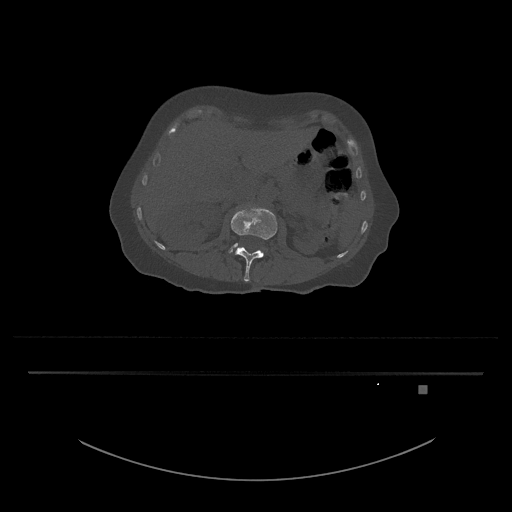
CT including the spine, one axial slice; slice 480 of 797 in the series (ordered by position); reconstruction kernel Br40s/3; bone window (W 1800 / L 400 HU); 0.5 mm slice thickness; 512 × 512 image matrix, field of view 500 × 500 mm. Patient: female, 57 years. Case-level facts recorded for this patient, not image findings: primary cancer: cervical.
Outlined on this slice (semi-automatically segmented with operator editing):
- L3 vertebra: box from (x=229, y=243) to (x=239, y=254) px